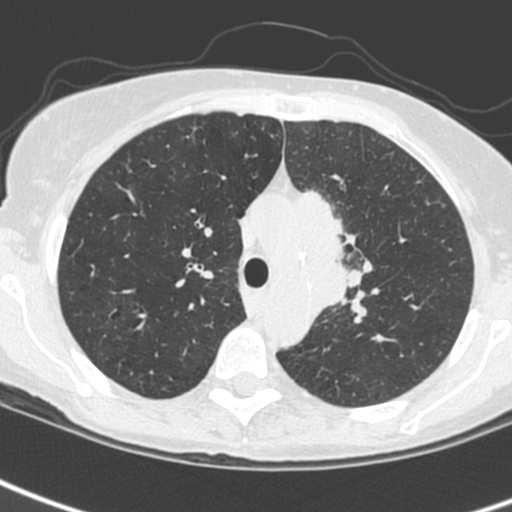
Low-dose screening chest CT, one axial slice; 120 kVp; lung window (W 1500 / L -600 HU); 512 × 512 image matrix, field of view 284 × 284 mm.
Structures marked on this image (manually delineated by an expert):
- lesion 3 (tumor, upper lobe of left lung): box from (x=296, y=190) to (x=351, y=314) px